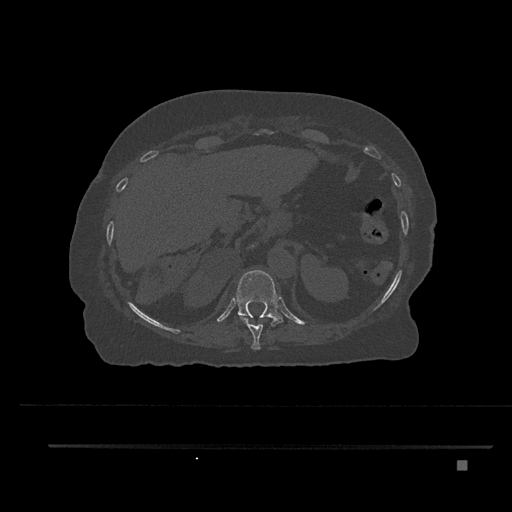
CT including the spine, one axial slice. Slice 327 of 797 in the series (ordered by position). 120 kVp. Bone window (W 1800 / L 400 HU). 512 × 512 image matrix, field of view 437 × 437 mm. Patient: female, 76 years. Case-level facts recorded for this patient, not image findings: primary cancer: lung.
Annotated regions visible in this slice (semi-automatic segmentation, software-assisted and operator-edited):
- T10 vertebra: box from (x=240, y=317) to (x=270, y=350) px
- T11 vertebra: (x=236, y=270)–(x=283, y=327)